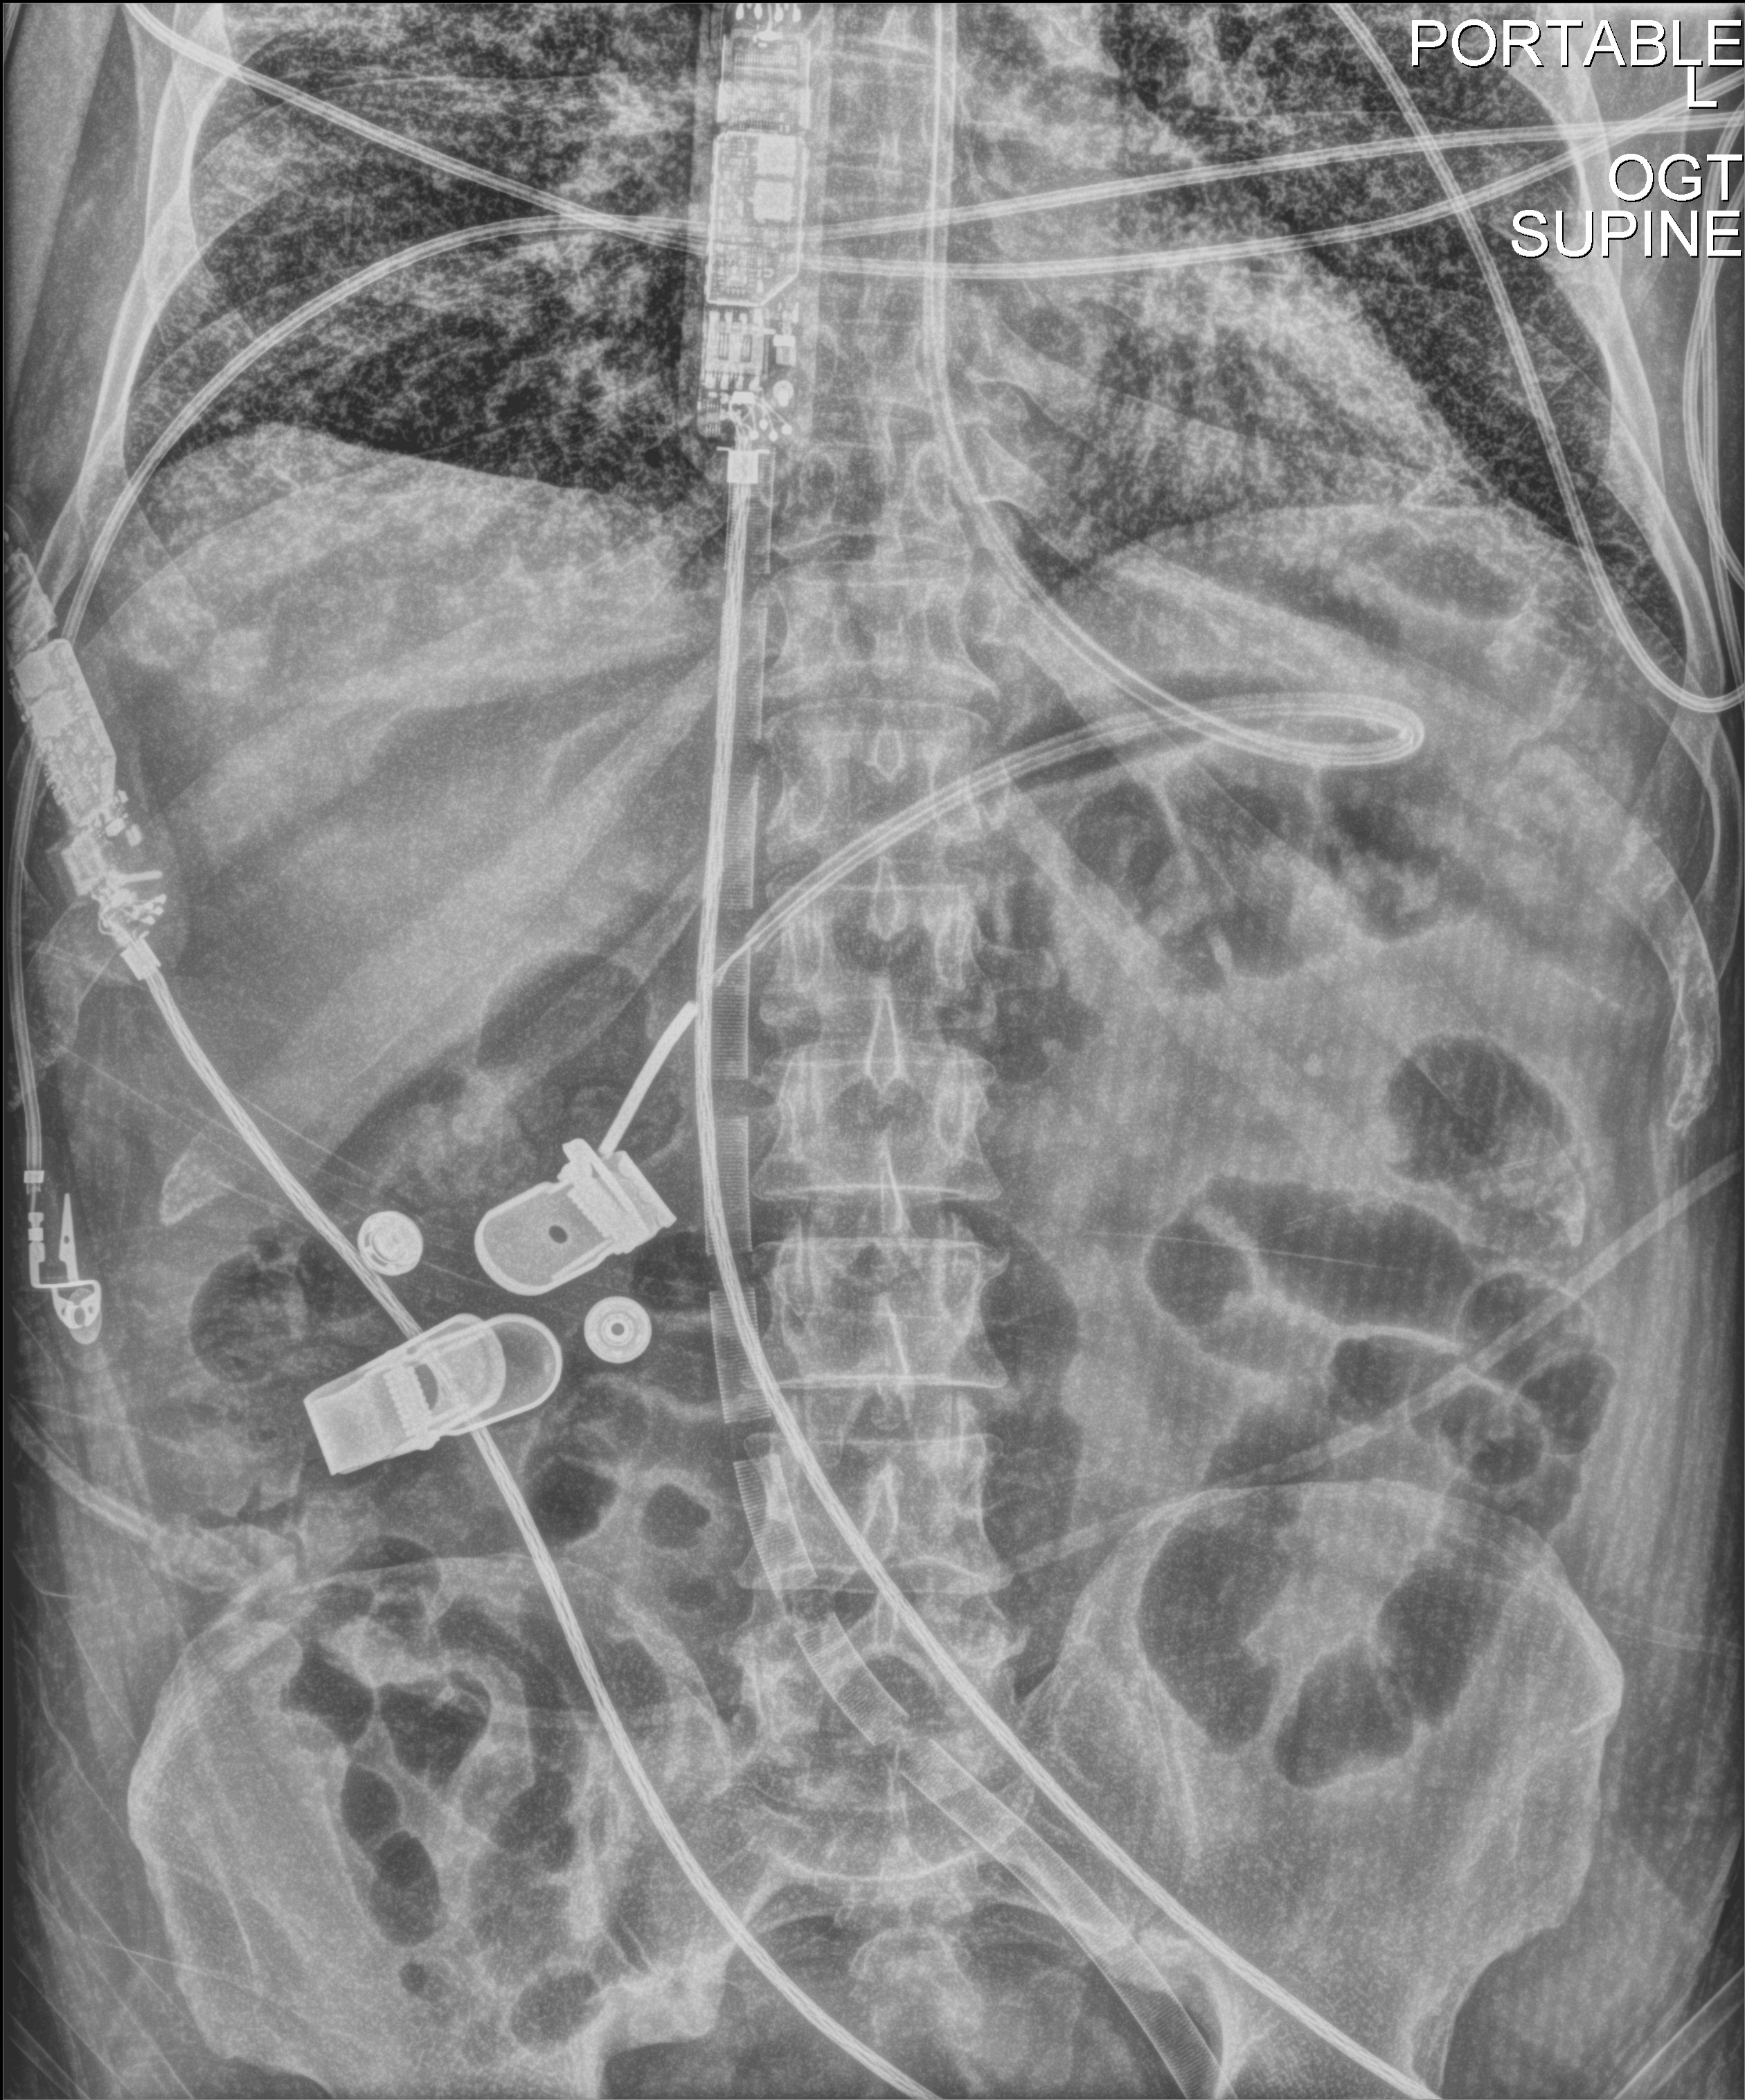
Abdomen radiograph (digital radiography); anteroposterior (AP) projection. Male patient hospitalised with COVID-19, age 18–59 years.
From the hospital-stay record, not from the radiograph (when in the stay this image was taken is not recorded):
- admitted to intensive care during this hospital stay: yes
- length of hospital stay: 42 days
- mechanically ventilated during this hospital stay: yes